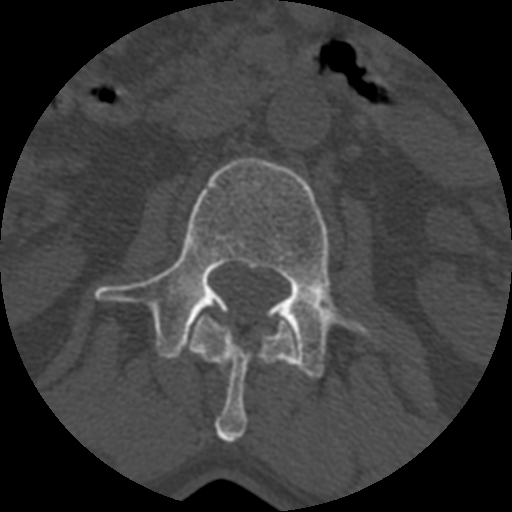
CT including the spine, one axial slice; slice 341 of 399 in the series (ordered by position); reconstruction kernel STANDARD; 120 kVp; bone window (W 1800 / L 400 HU); 1.25 mm slice thickness; 512 × 512 image matrix, field of view 160 × 160 mm. Patient age 71 years. Case-level facts recorded for this patient, not image findings: primary cancer: prostate.
Annotated regions visible in this slice (semi-automatic segmentation, software-assisted and operator-edited):
- L1 vertebra: box from (x=188, y=309) to (x=296, y=443) px
- L2 vertebra: (x=95, y=158)–(x=382, y=379)